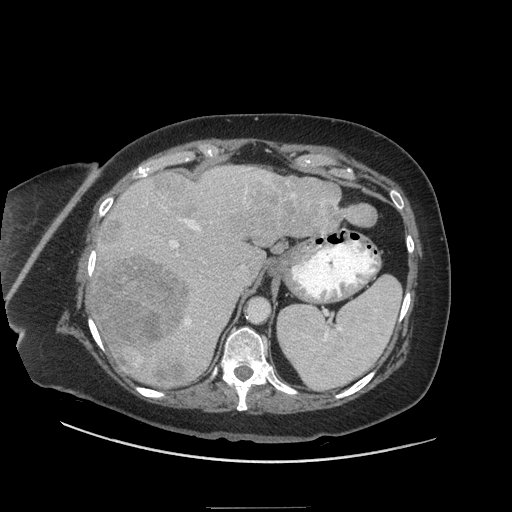
Contrast-enhanced abdominal CT (liver protocol), one axial slice. Position 41 of 81 along the scan axis. 140 kVp. Soft-tissue window (W 400 / L 40 HU). 2.5 mm slice thickness. 512 × 512 image matrix, field of view 440 × 440 mm. From the clinical record (not read from this slice): diagnosis: hepatocellular carcinoma (patient treated with transarterial chemoembolisation; whether this scan precedes or follows treatment is not stated here); TNM stage (as recorded): Stage-II; Child-Pugh class: A; tumour nodularity: multinodular; tumour size: 1.7 cm.
Structures marked on this image (semi-automatically segmented with operator editing):
- liver parenchyma outside the tumour (the mass and vessels are separate outlines, so this box may not span the whole liver): bounding box <88,166,367,388> (left, top, right, bottom; pixels)
- mass: <89,173,375,387>
- liver vessels: <134,169,270,367>